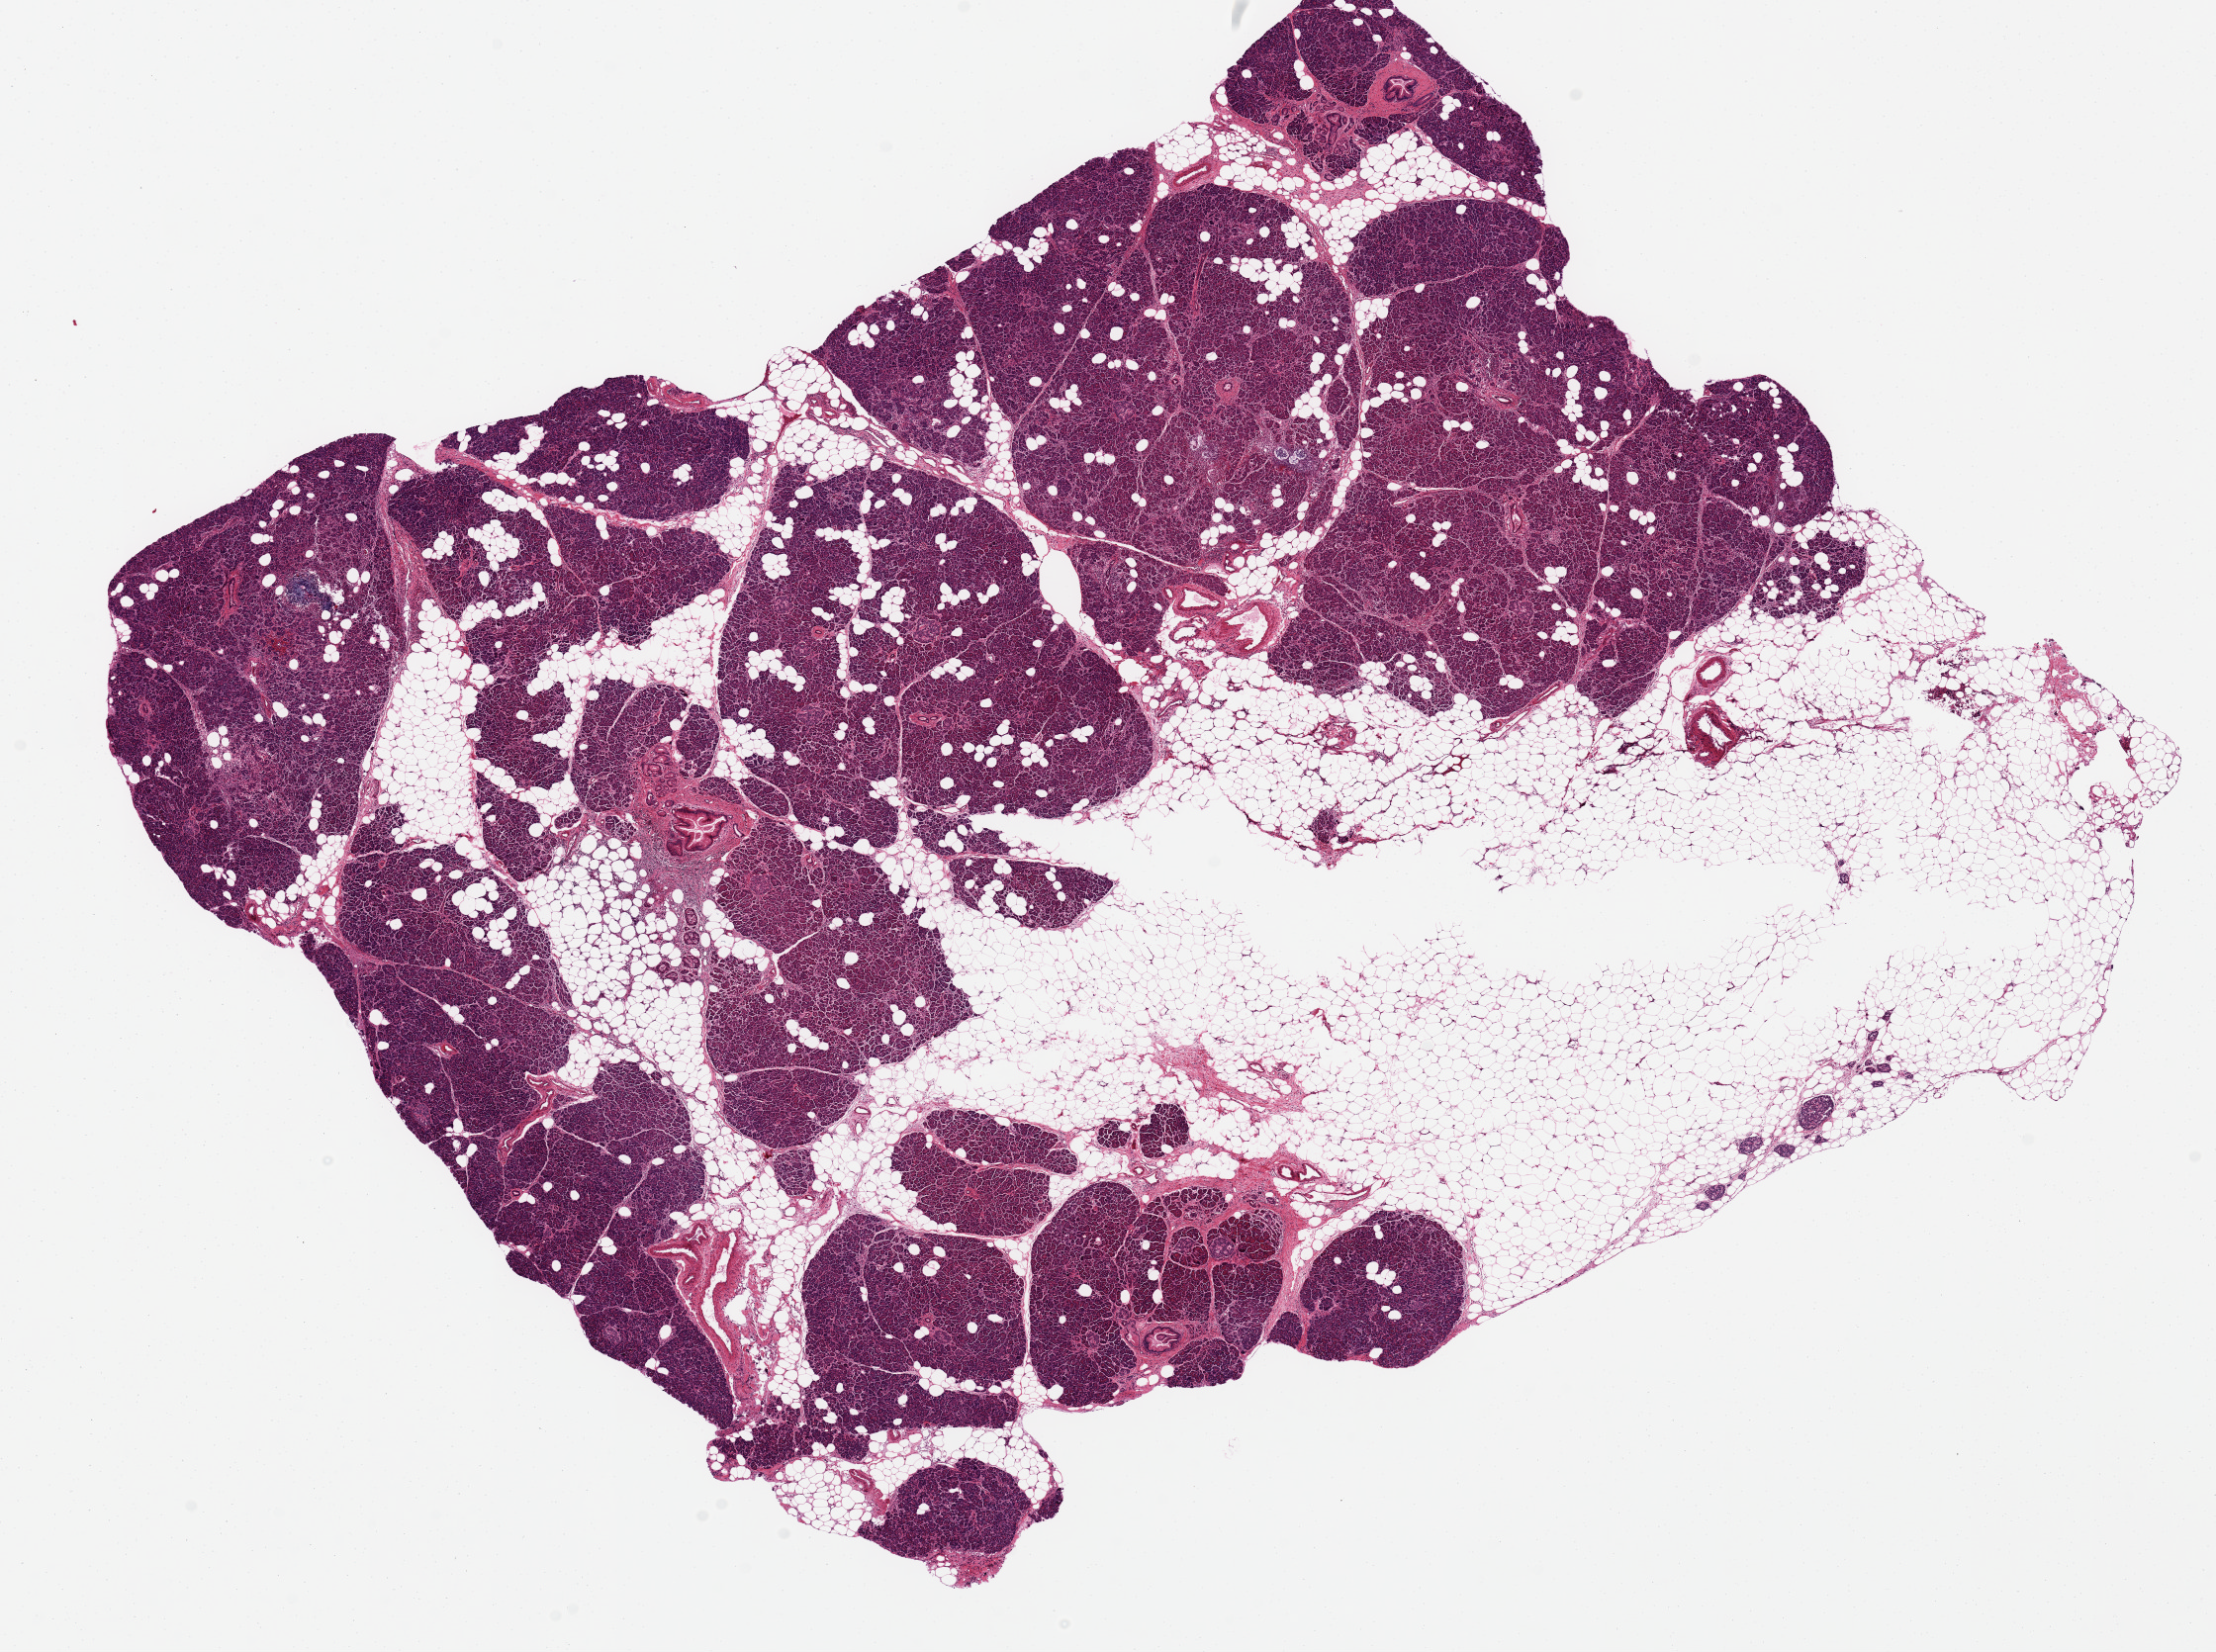
Whole-slide image, hematoxylin and eosin (H&E) stain, brightfield, whole scanned area (about 17.7 x 13.2 mm) shown as a low-resolution overview, PAXgene-fixed paraffin-embedded (PFPE) section, sampled site (target tissue): pancreas, donor tissue sample. Donor sex: male.
- pathologist's review note for this sample: Well preserved pancreas with about 40% fat in aliquot